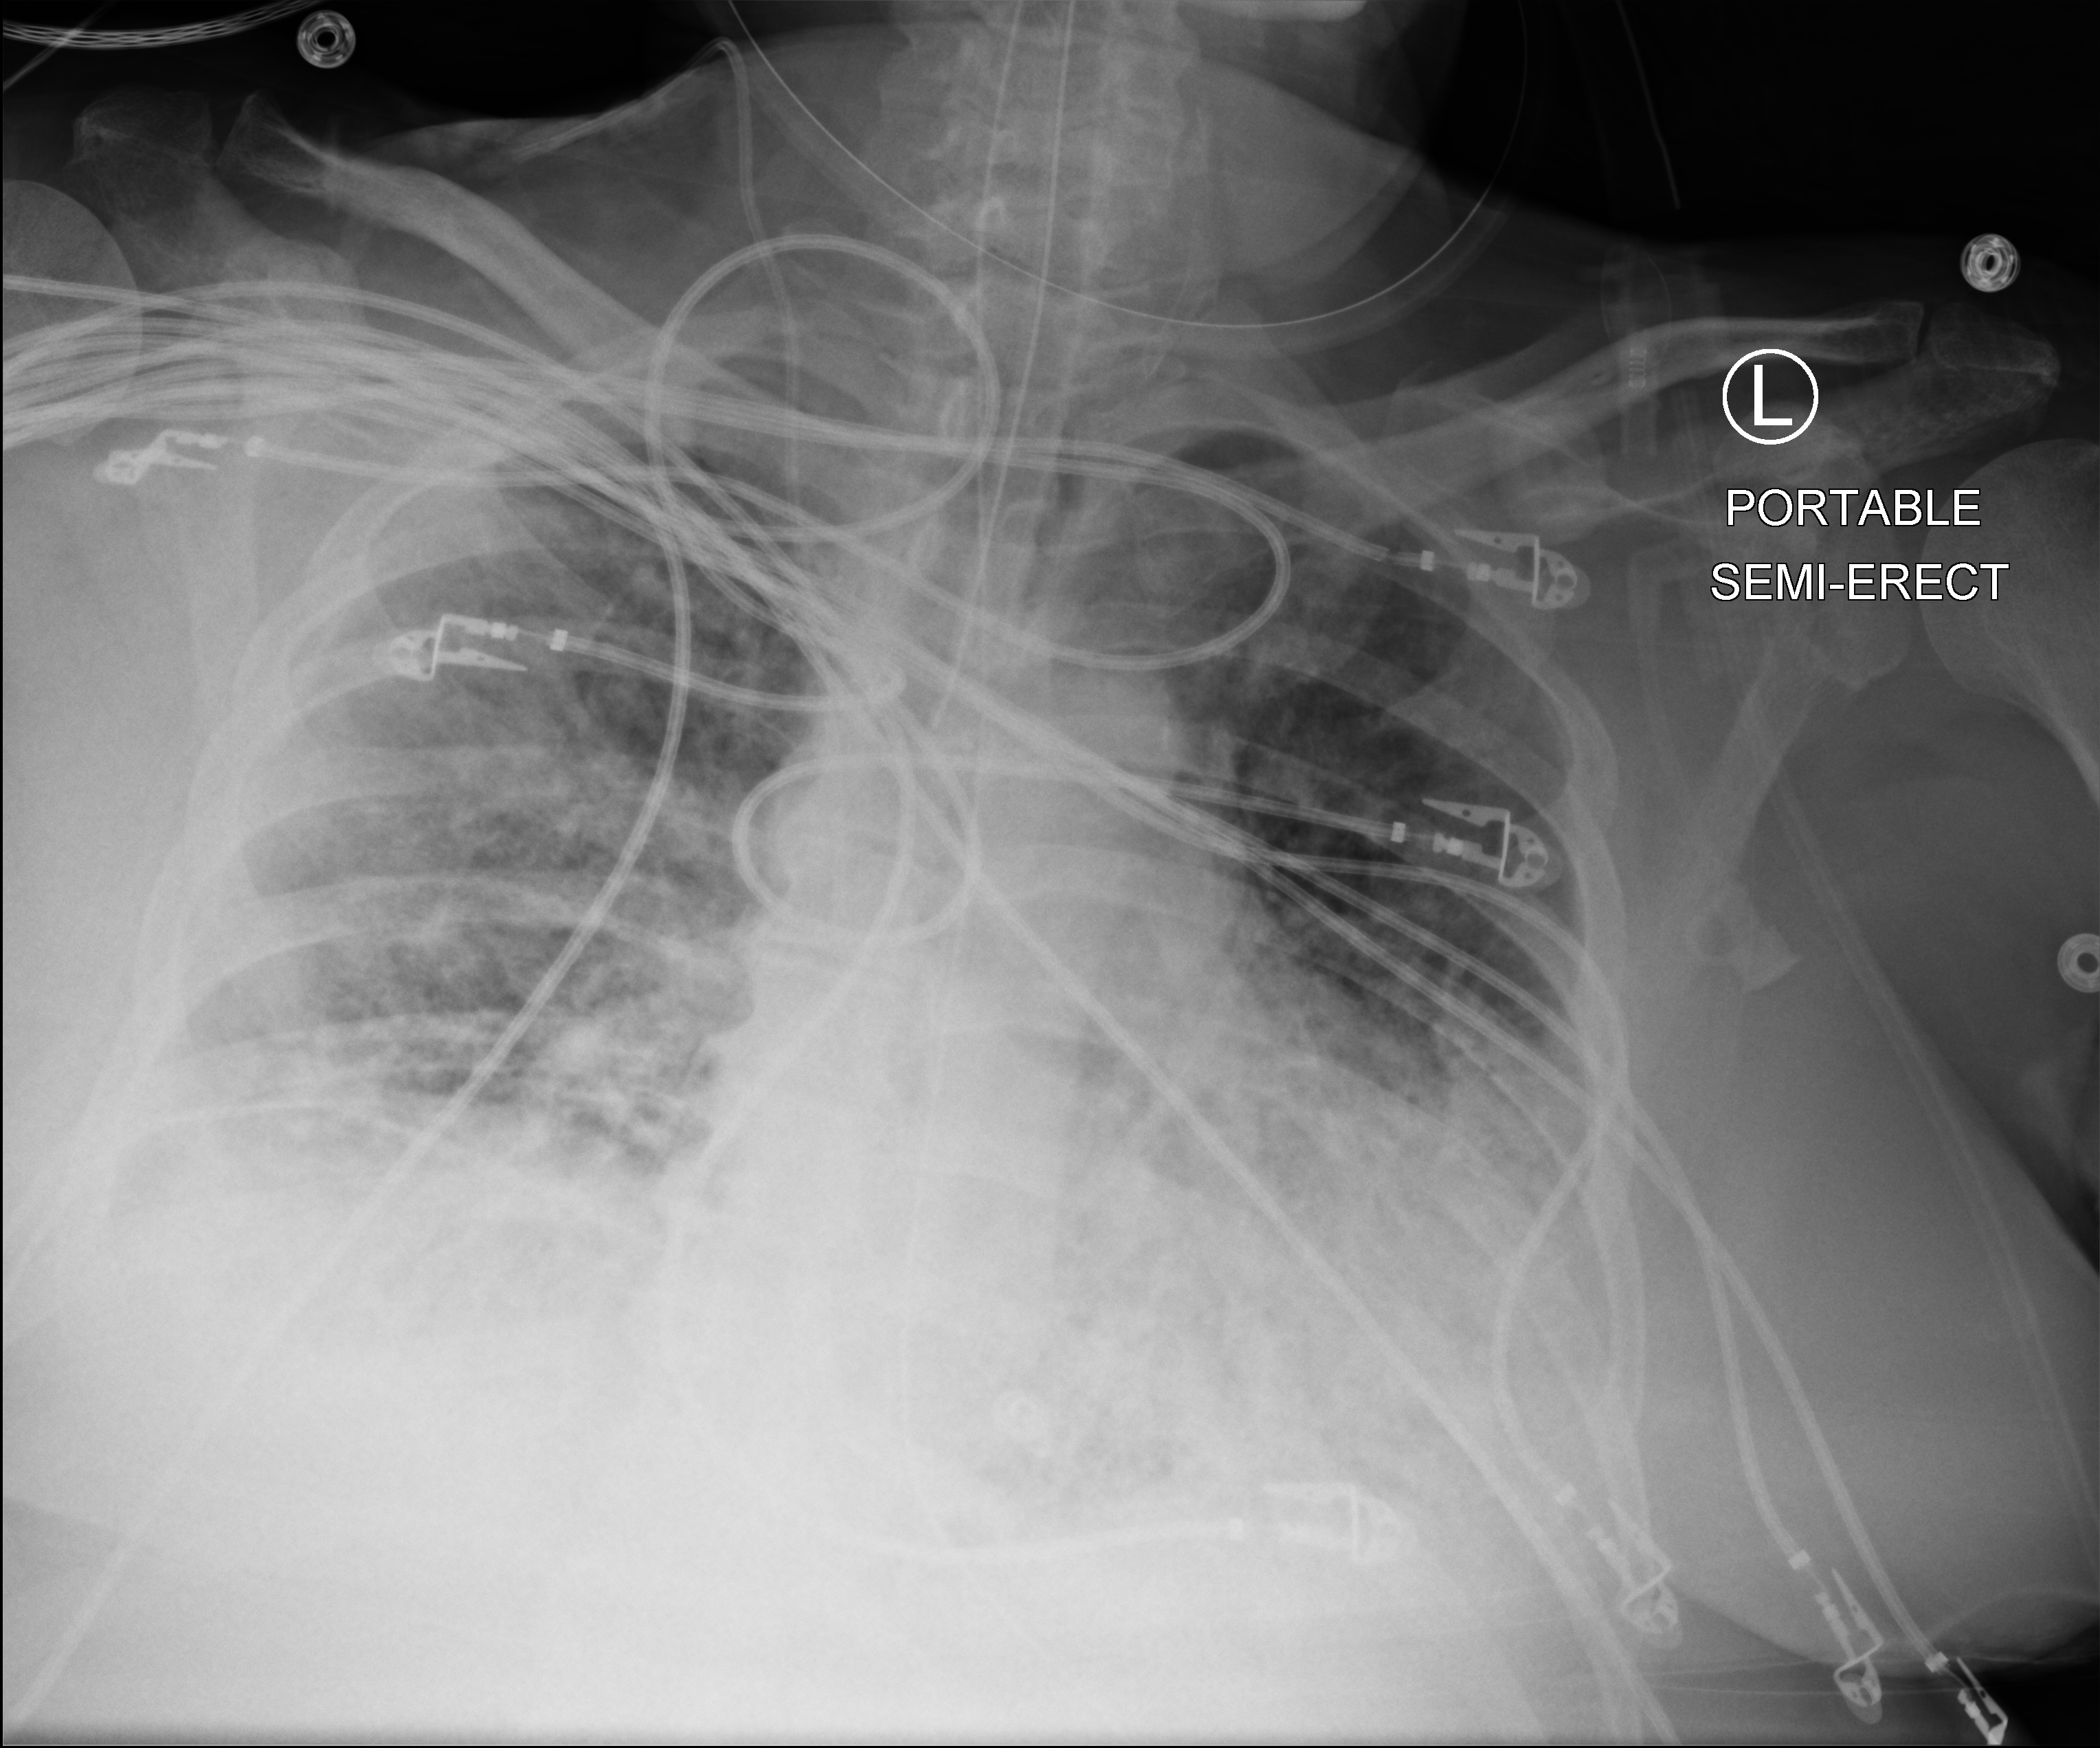
Chest X-ray (portable), anteroposterior (AP) projection. Male patient hospitalised with COVID-19, age 60–74 years.
Admission-level facts for this patient (not findings on this image; timing relative to this image not recorded):
- hypertension (admission record): yes
- admitted to intensive care during this hospital stay: yes